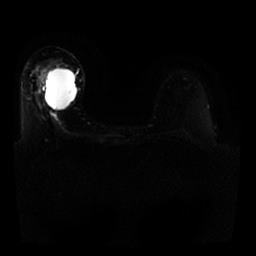
Breast MRI, one axial slice; slice 15 of 25 in the series (ordered by position); diffusion-weighted series; image 2 of 4 stored at this slice position (different b-values; order by instance number); 1.5 T; 4 mm slice thickness; 256 × 256 image matrix, field of view 330 × 330 mm. Female patient.
Annotated regions visible in this slice (outlined manually by an expert reader):
- tumour on diffusion-weighted imaging: box from (x=45, y=69) to (x=52, y=82) px